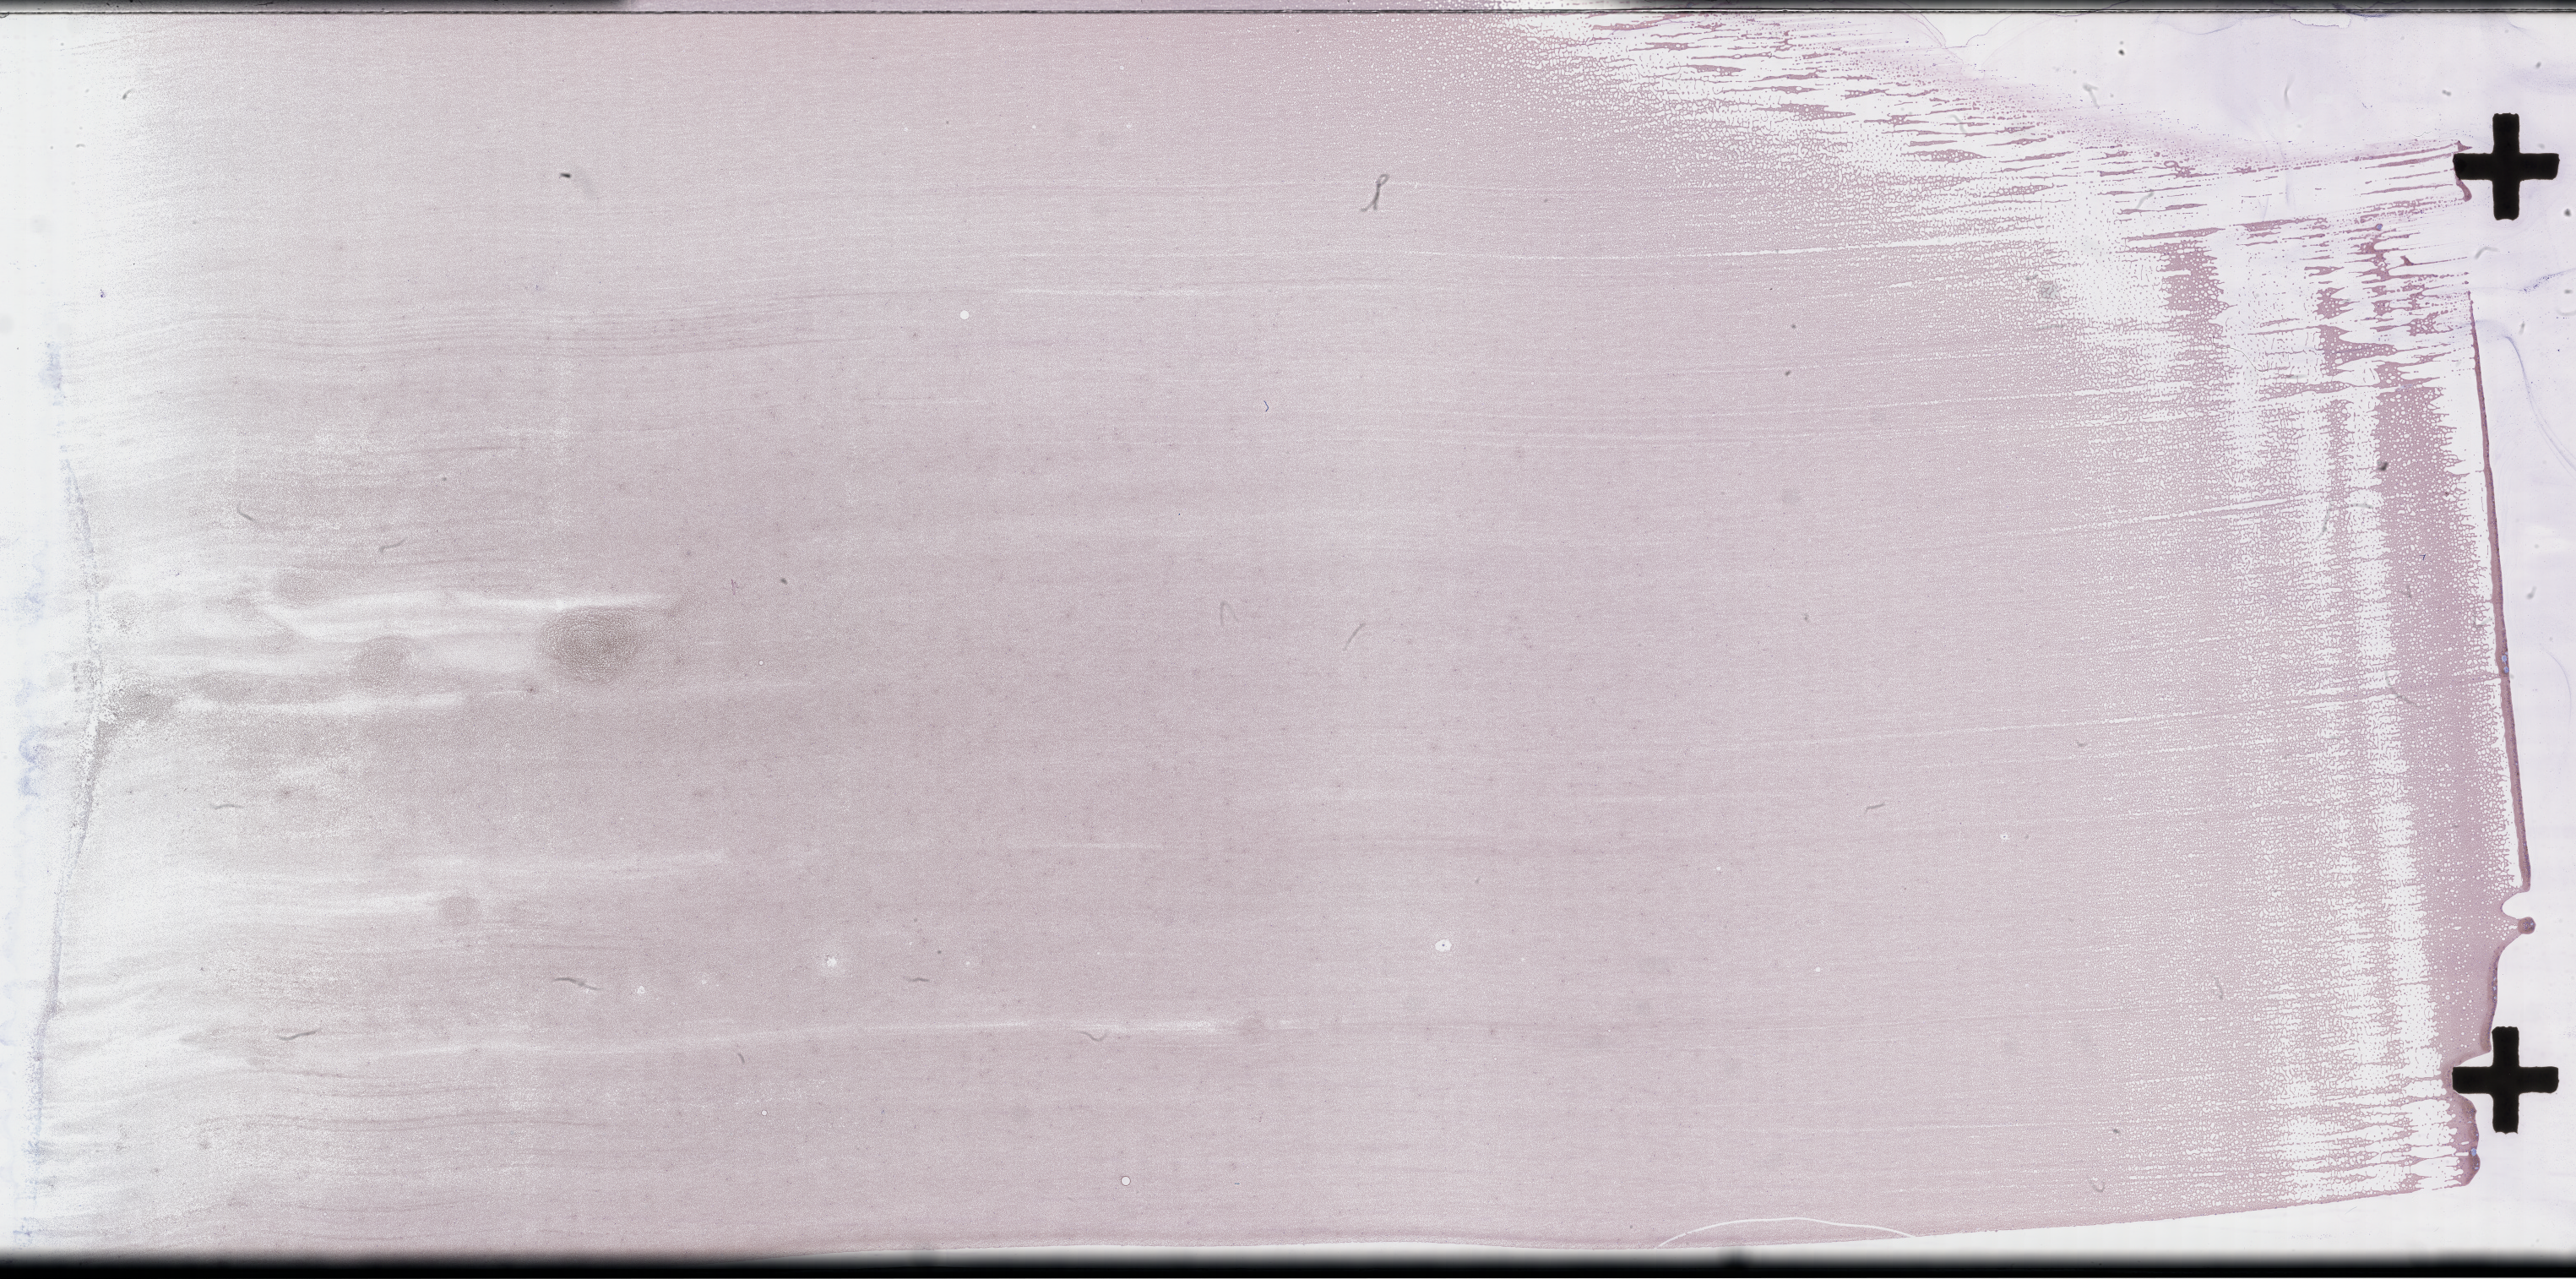
Wright-Giemsa-stained whole blood smear, whole-slide image, low-resolution overview of the scanned area, about 49.3 x 24.4 mm. Patient: female.
- patient diagnosis: Plasma Cell Myeloma